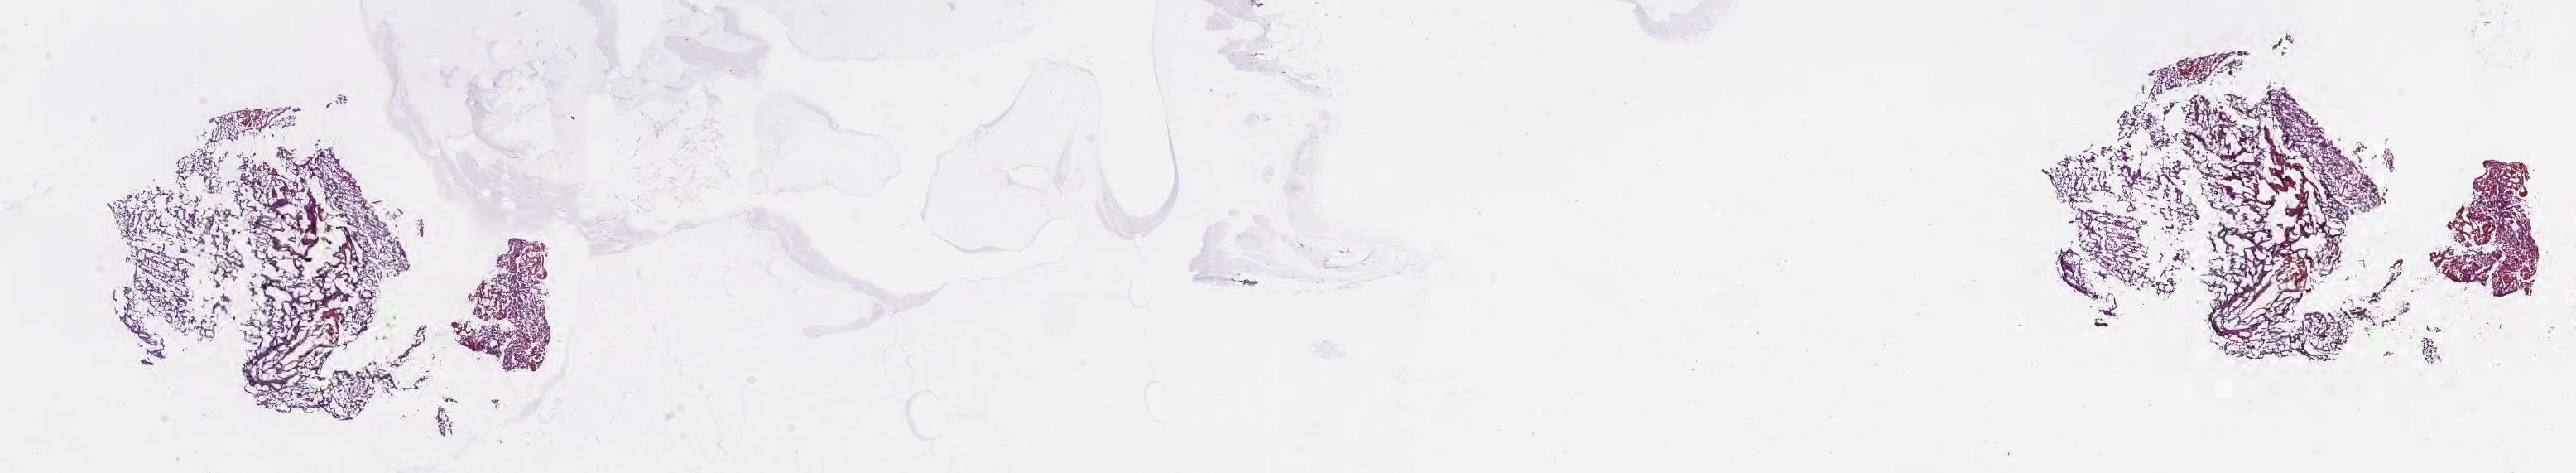
H&E whole-slide image of tumor tissue from the temporal lobe — a low-resolution overview of the entire scanned area, about 25.2 x 4.6 mm, frozen section. Patient: female, age 197 months (16 years 5 months).
Recorded diagnosis: Astrocytoma, NOS.